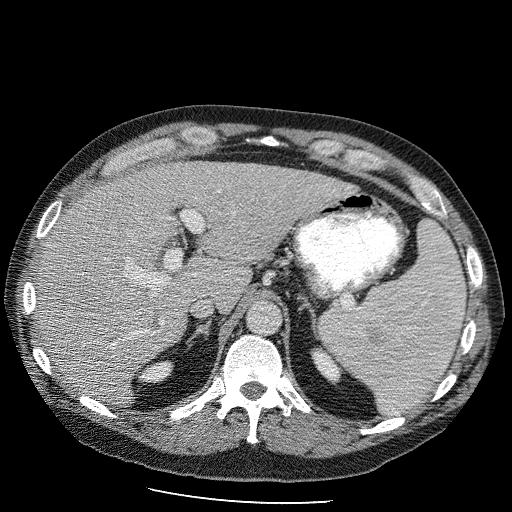
Contrast-enhanced abdominal CT (liver protocol), one axial slice. Slice 68 of 98 in the series (ordered by position). Reconstruction kernel STANDARD. Soft-tissue window (W 400 / L 40 HU). 2.5 mm slice thickness. 512 × 512 image matrix, field of view 400 × 400 mm. Case-level facts recorded for this patient, not image findings: diagnosis: hepatocellular carcinoma (patient treated with transarterial chemoembolisation; whether this scan precedes or follows treatment is not stated here); TNM stage (as recorded): Stage-II; Child-Pugh class: B; tumour differentiation: moderately differentiated; tumour nodularity: uninodular.
Structures marked on this image (semi-automatic segmentation, software-assisted and operator-edited):
- liver parenchyma outside the tumour (the mass and vessels are separate outlines, so this box may not span the whole liver): bounding box (x1, y1, x2, y2) in pixels: (35, 160, 351, 406)
- liver vessels: (124, 218, 204, 334)